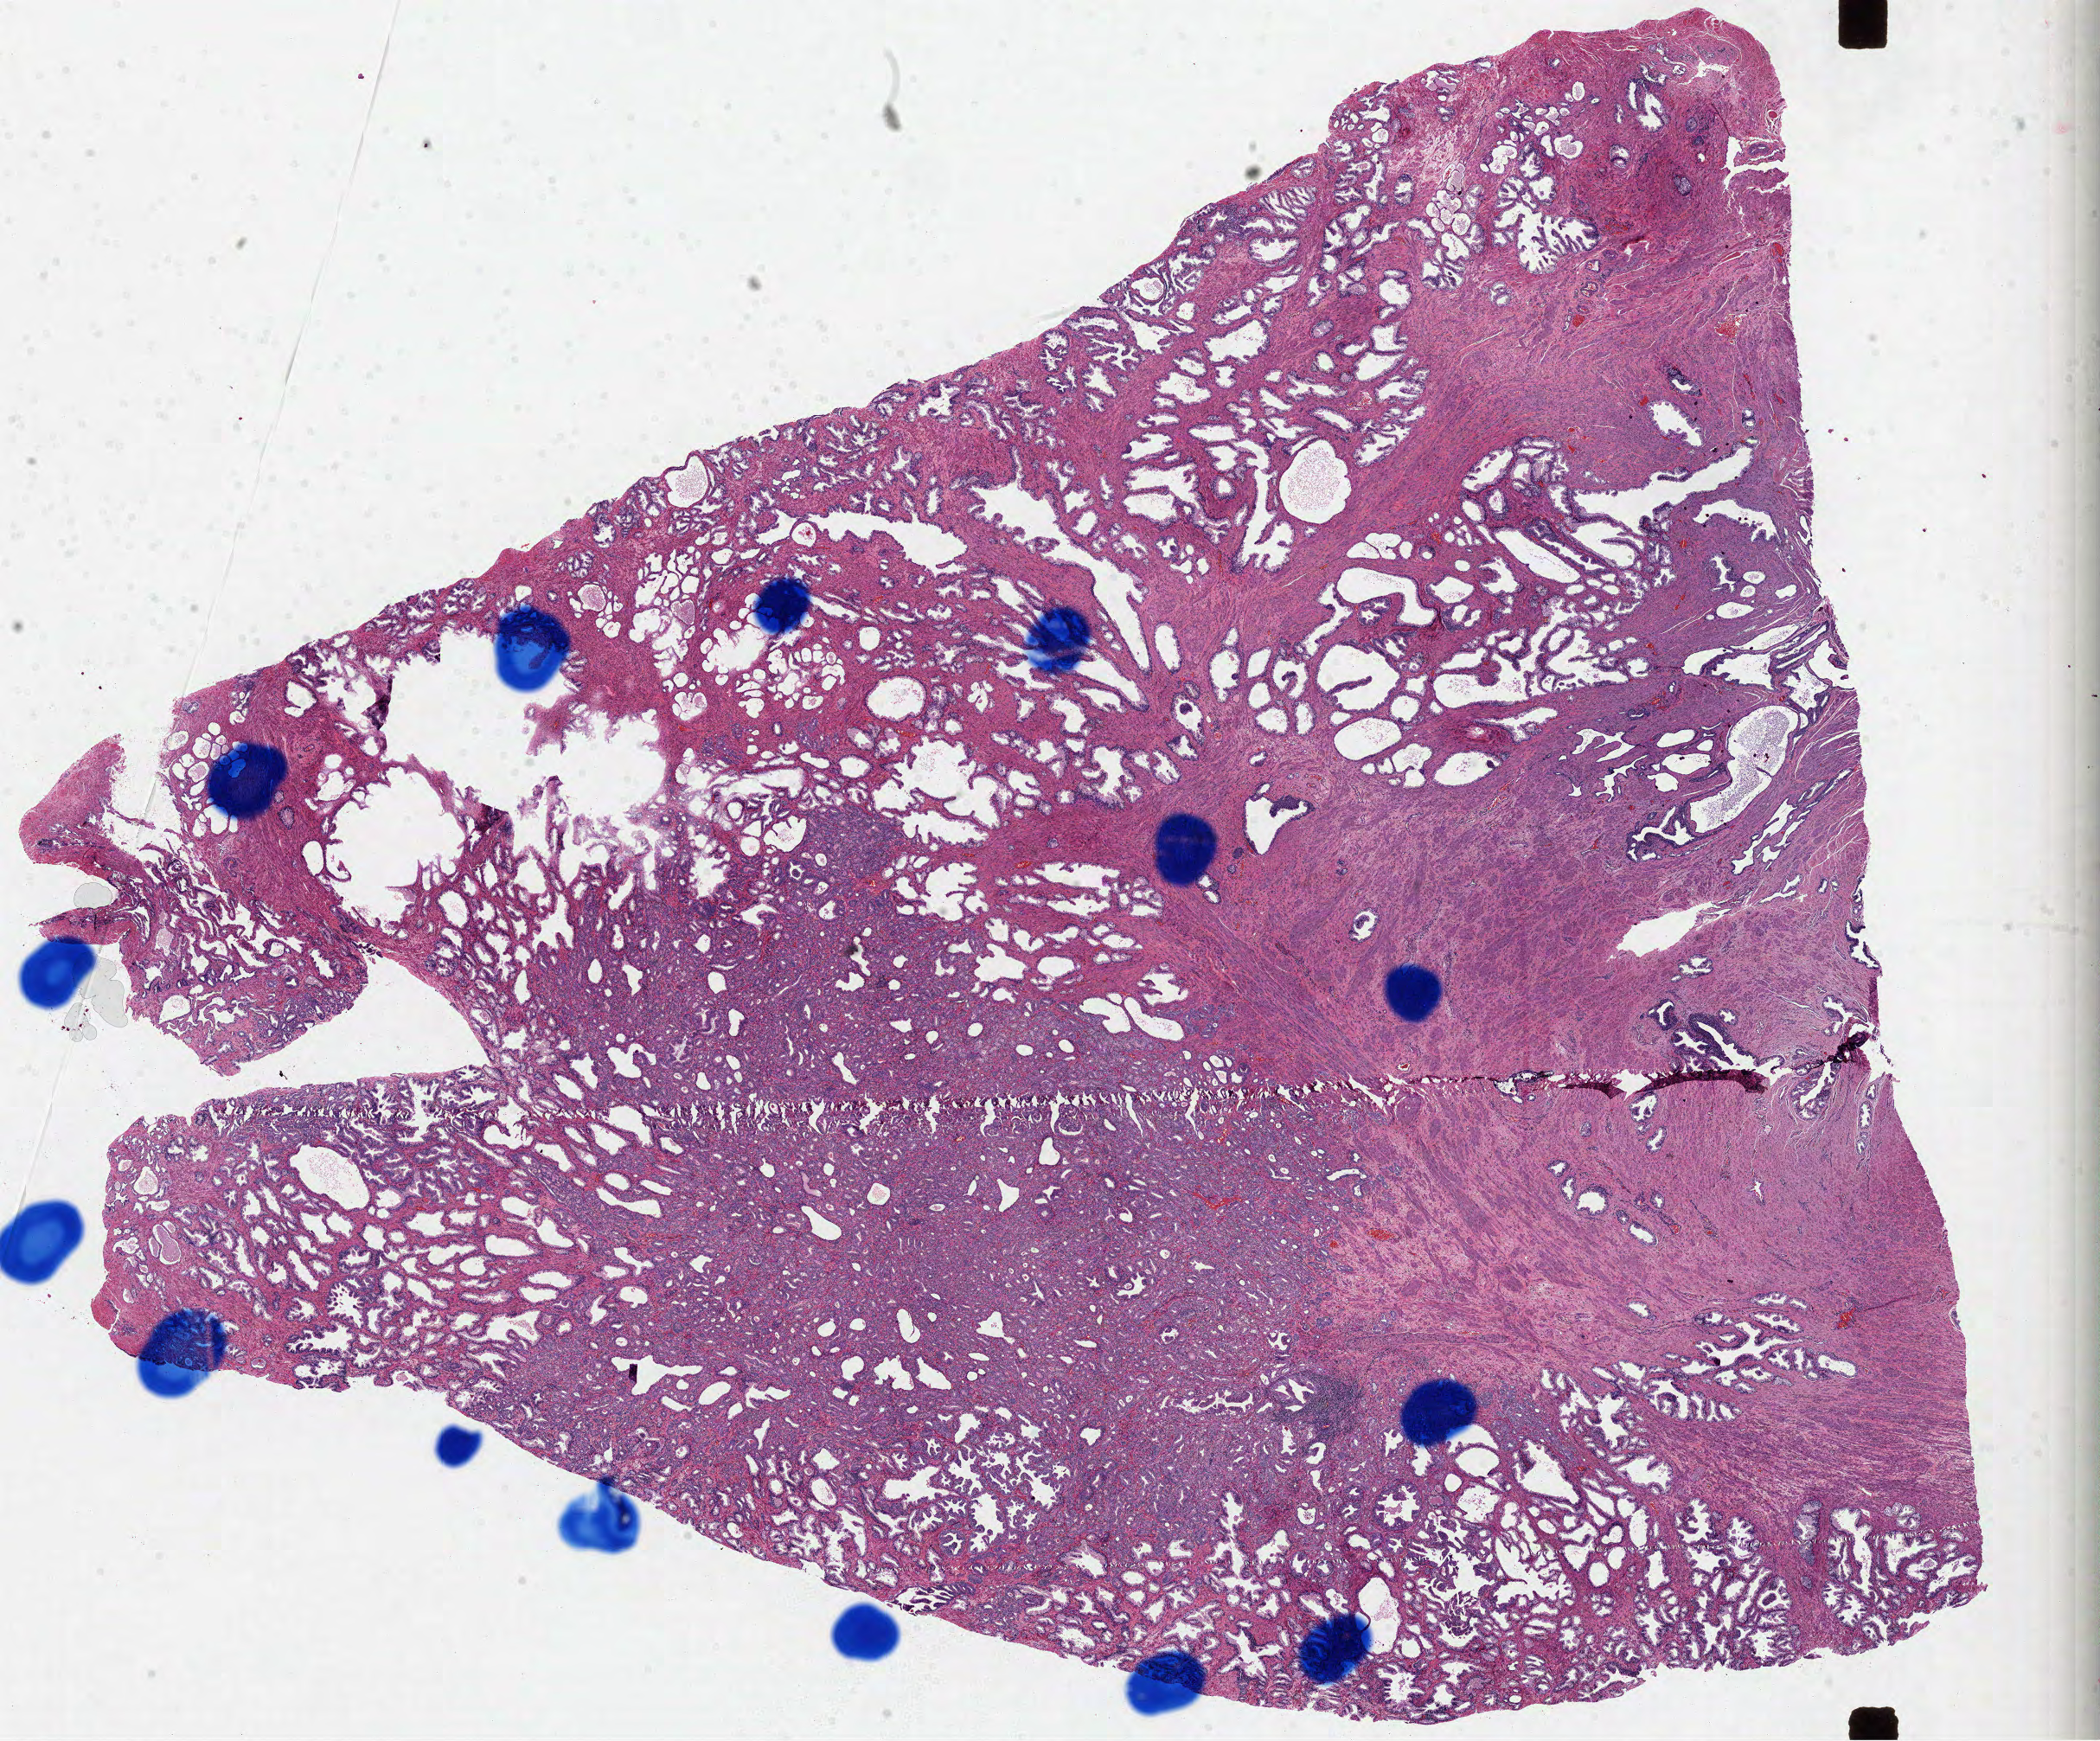
H&E whole-slide image, a low-resolution overview of the entire scanned area, about 19.6 x 16.2 mm (from a 40x scan); formalin-fixed paraffin-embedded (FFPE) diagnostic section; prostate, primary tumour sample. Patient: male, age at initial diagnosis 57 years. Gleason score: 7 (4+3).
Histologic diagnosis: Acinar cell carcinoma (prostate gland).